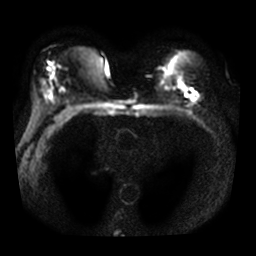
Breast MRI, one axial slice. Position 18 of 32 along the scan axis. Diffusion-weighted series; image 2 of 4 stored at this slice position (different b-values; order by instance number). 3 T. 5 mm slice thickness. 256 × 256 image matrix, field of view 320 × 320 mm. Female patient.
Structures marked on this image (outlined manually by an expert reader):
- tumour on diffusion-weighted imaging: bounding box (x1, y1, x2, y2) in pixels: (192, 93, 198, 100)